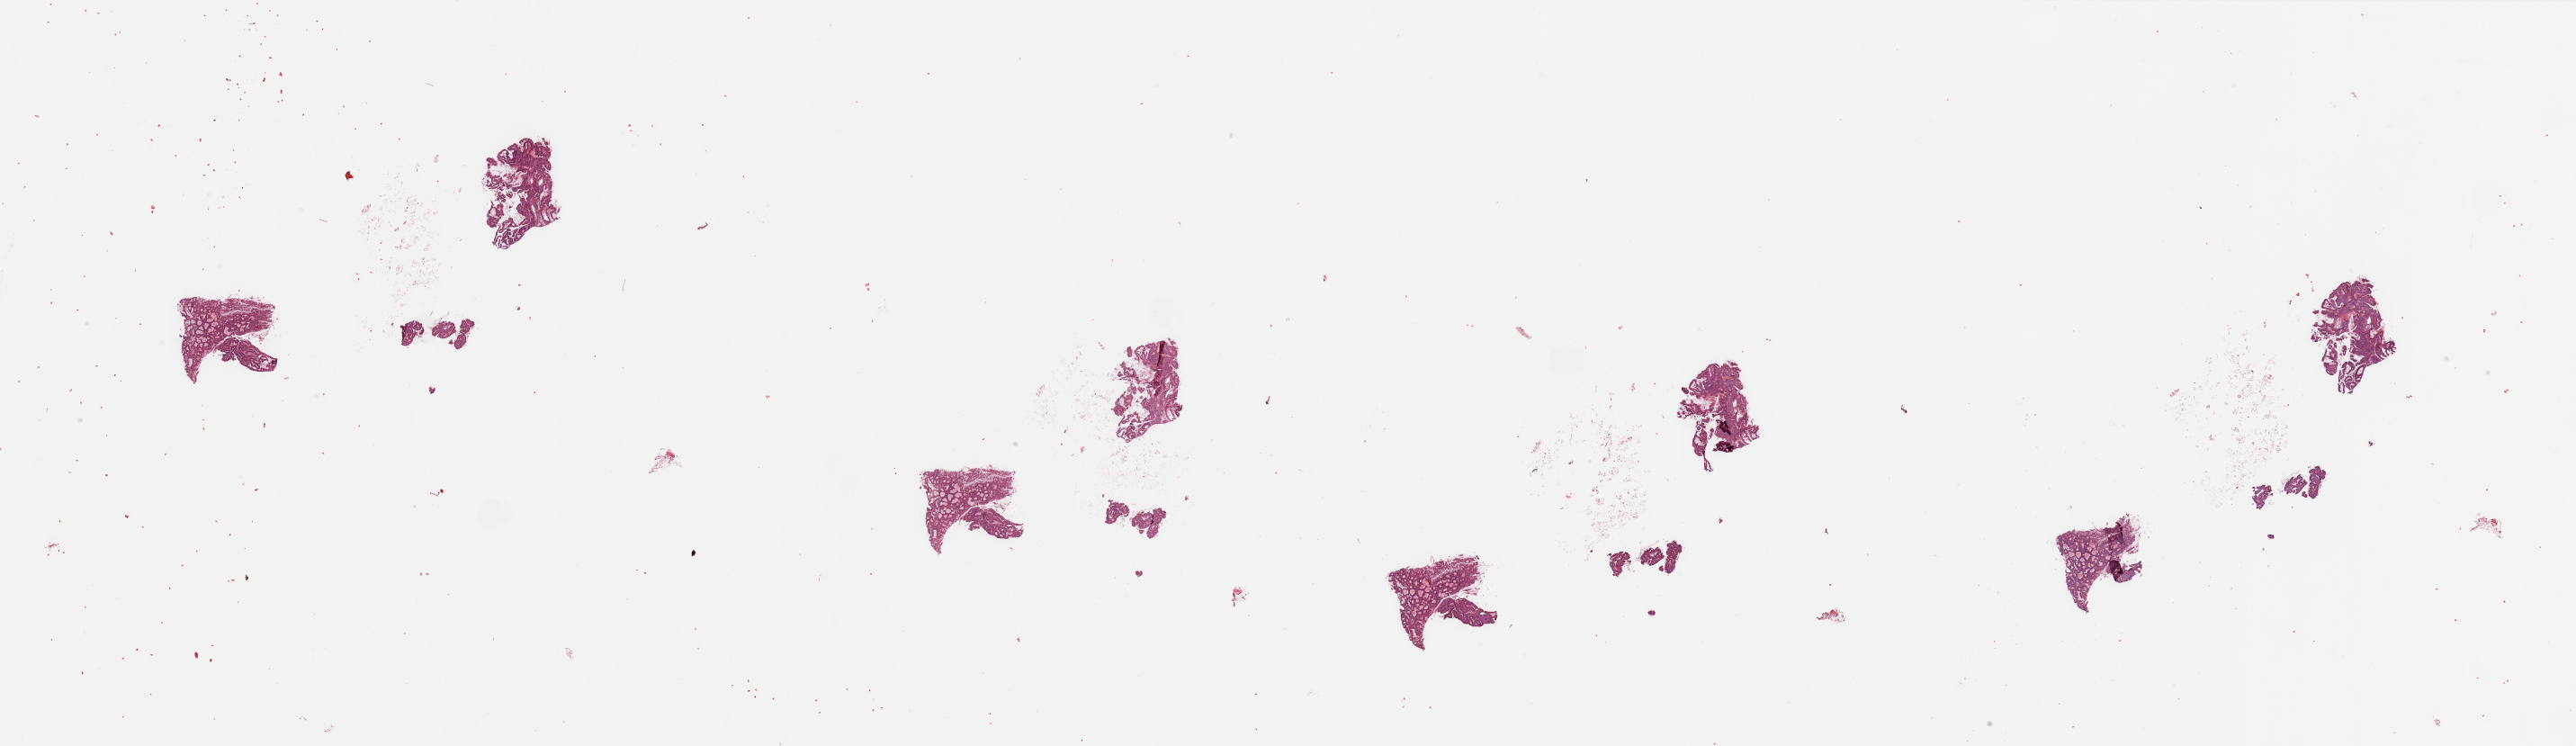
Hematoxylin and eosin (H&E) stained whole-slide image, a low-resolution overview of the entire scanned area, about 45.3 x 13.1 mm (from a 20x scan). Tumour tissue sample, sampled site: uterus. Female, 77 y/o. Histologic grade: G2 (moderately differentiated). Slide review estimates, as recorded: tumour nuclei 90%, necrosis 2%.
Primary tumour site (as recorded): anterior endometrium. Histologic diagnosis: Endometrioid adenocarcinoma, NOS. AJCC pathologic stage: I.